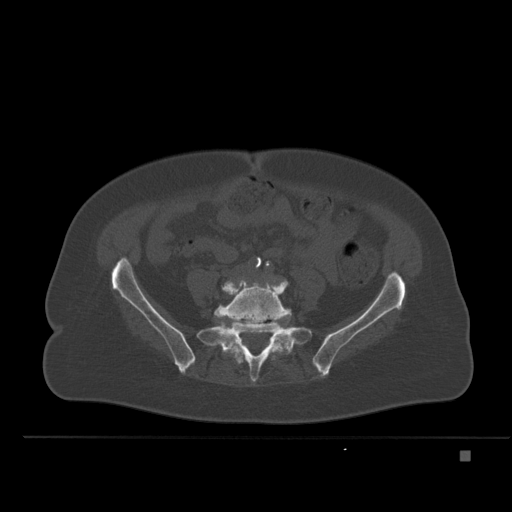
CT including the spine, one axial slice. Position 155 of 477 along the scan axis. Bone window (W 1800 / L 400 HU). 1.5 mm slice thickness. 512 × 512 image matrix. Female patient, age 74 years. From the clinical record (not read from this slice): primary cancer: colon.
Structures marked on this image (semi-automatic segmentation, software-assisted and operator-edited):
- L5 vertebra: bounding box (x1, y1, x2, y2) in pixels: (215, 280, 291, 363)